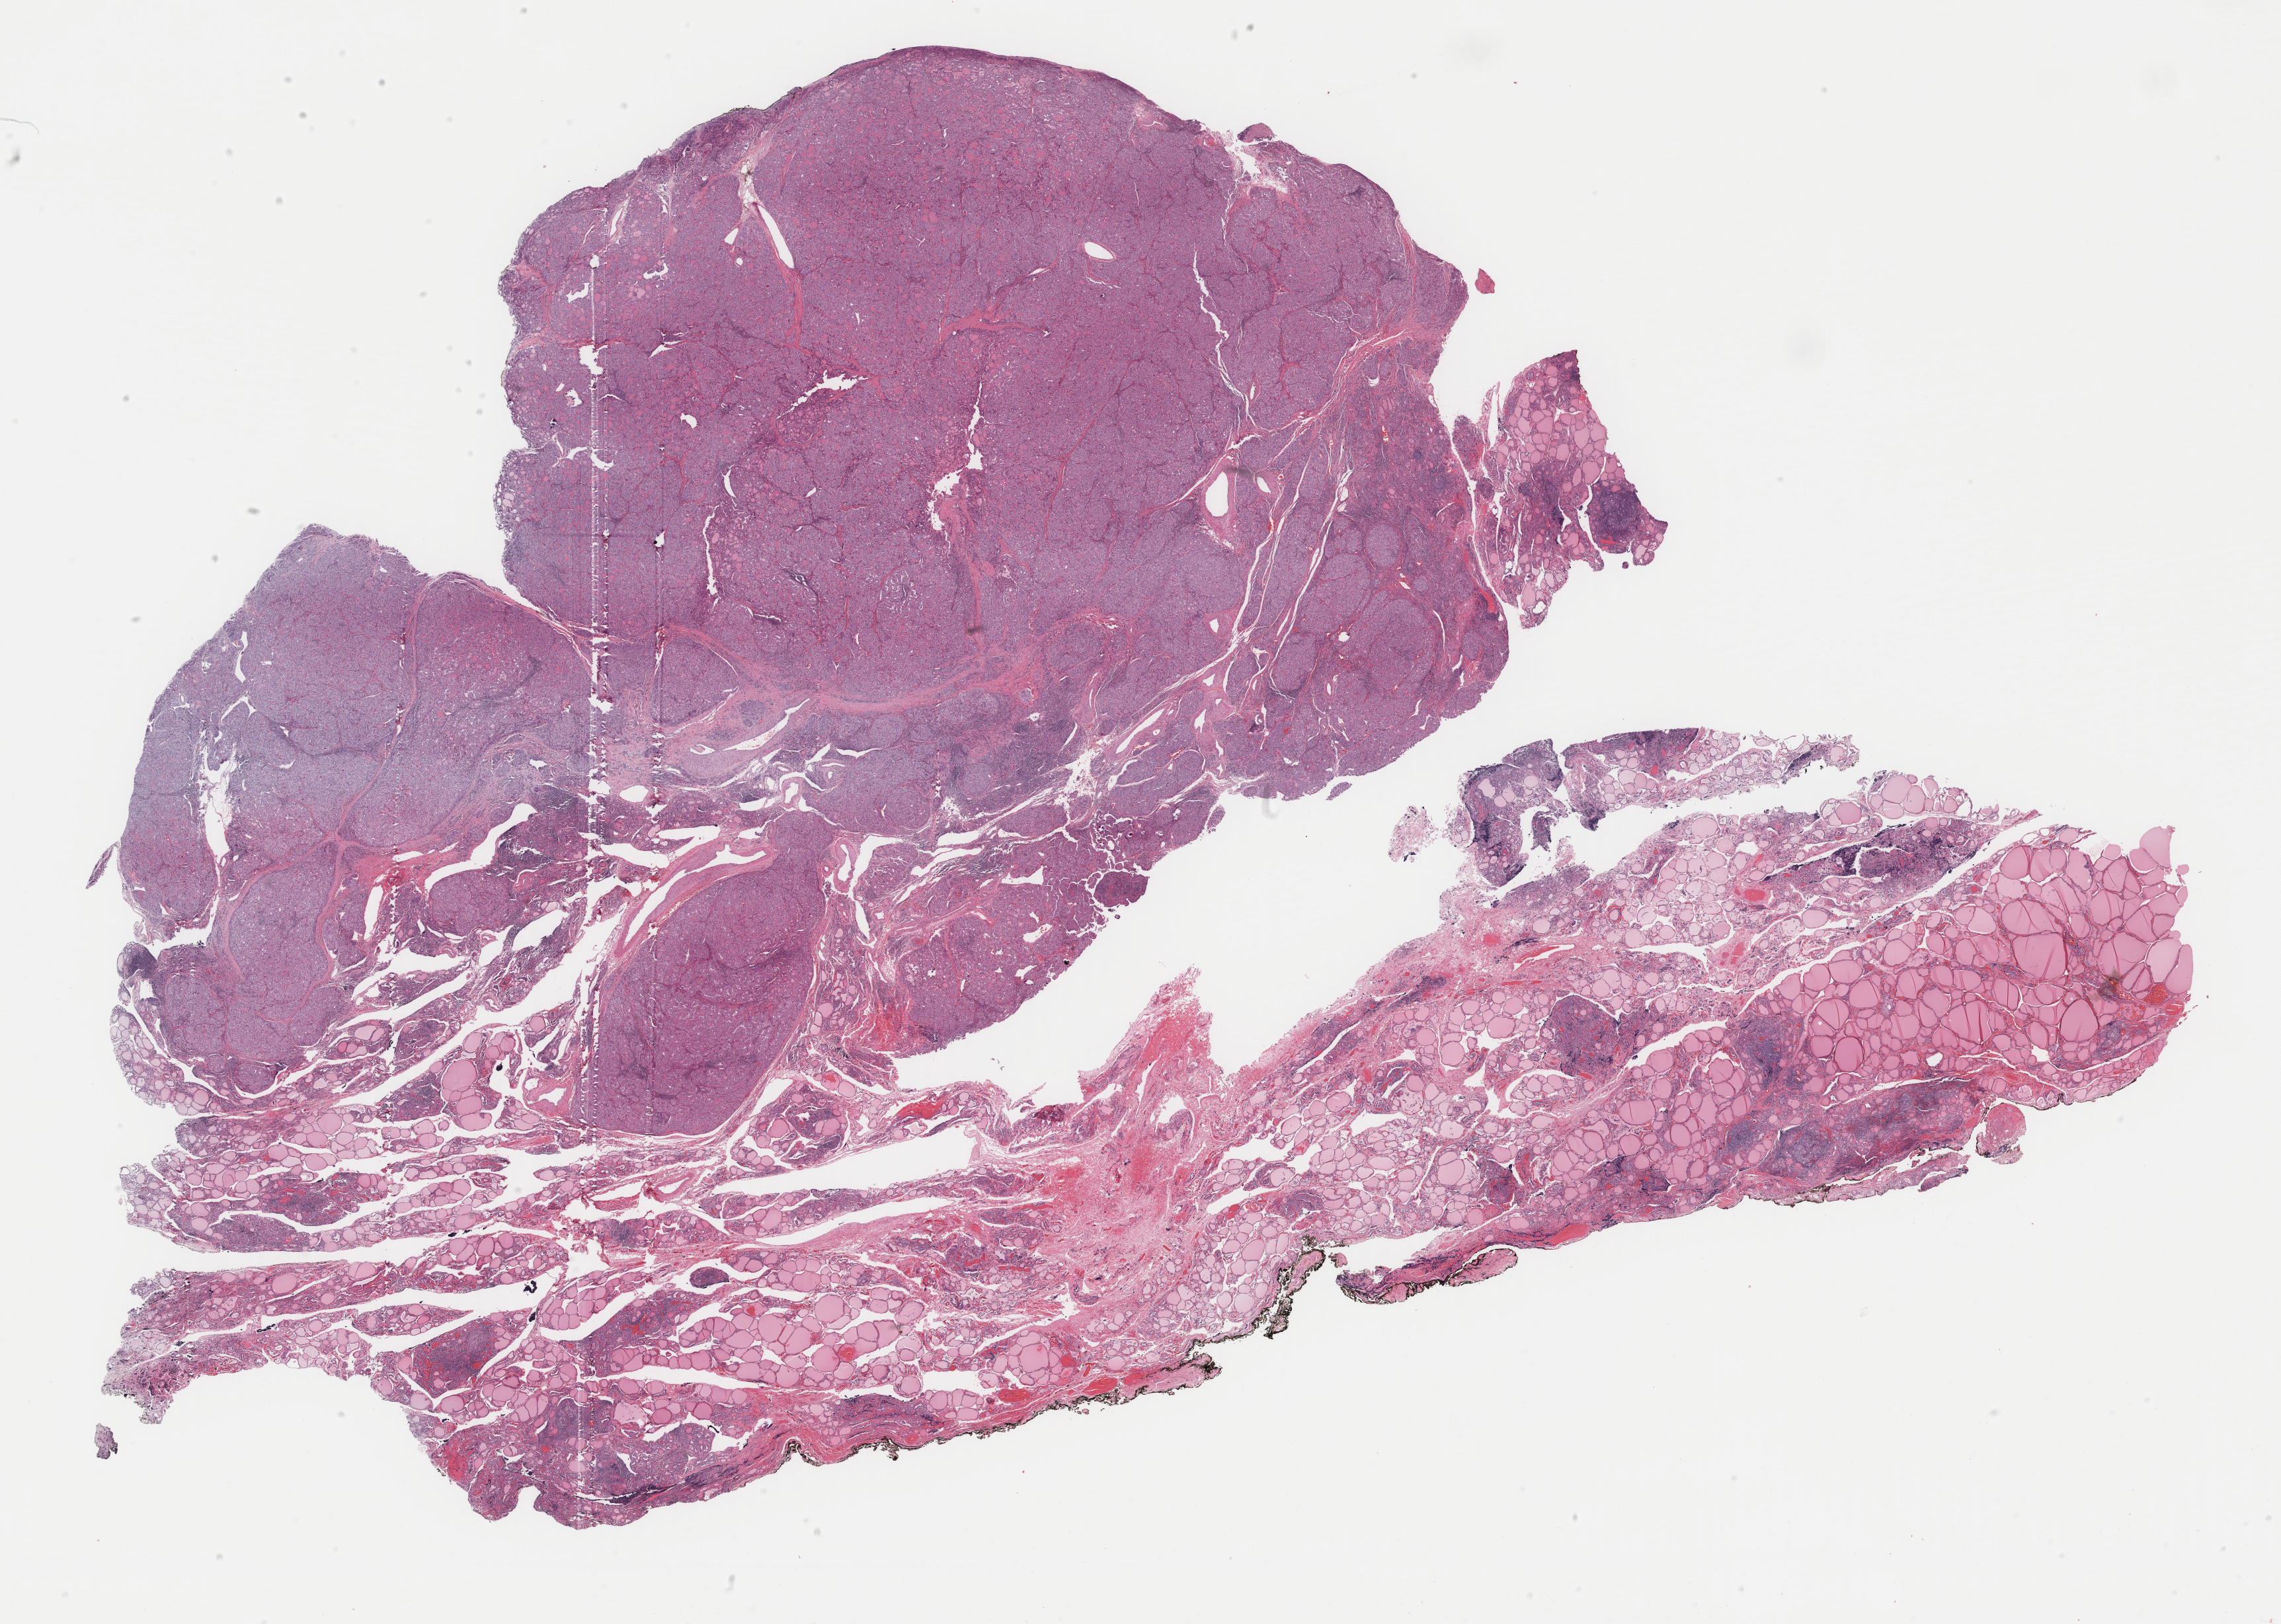
H&E-stained whole-slide image, shown as a low-resolution overview of the whole scanned area (about 27.4 x 19.5 mm, acquisition: 40x scan); FFPE section; sample: primary tumour, thyroid. Patient: female, age at initial diagnosis 17 years.
Histologic diagnosis: Papillary carcinoma, follicular variant. Lymph nodes positive (case pathology): 0 of 3 examined. AJCC pathologic stage: I (6th edition).